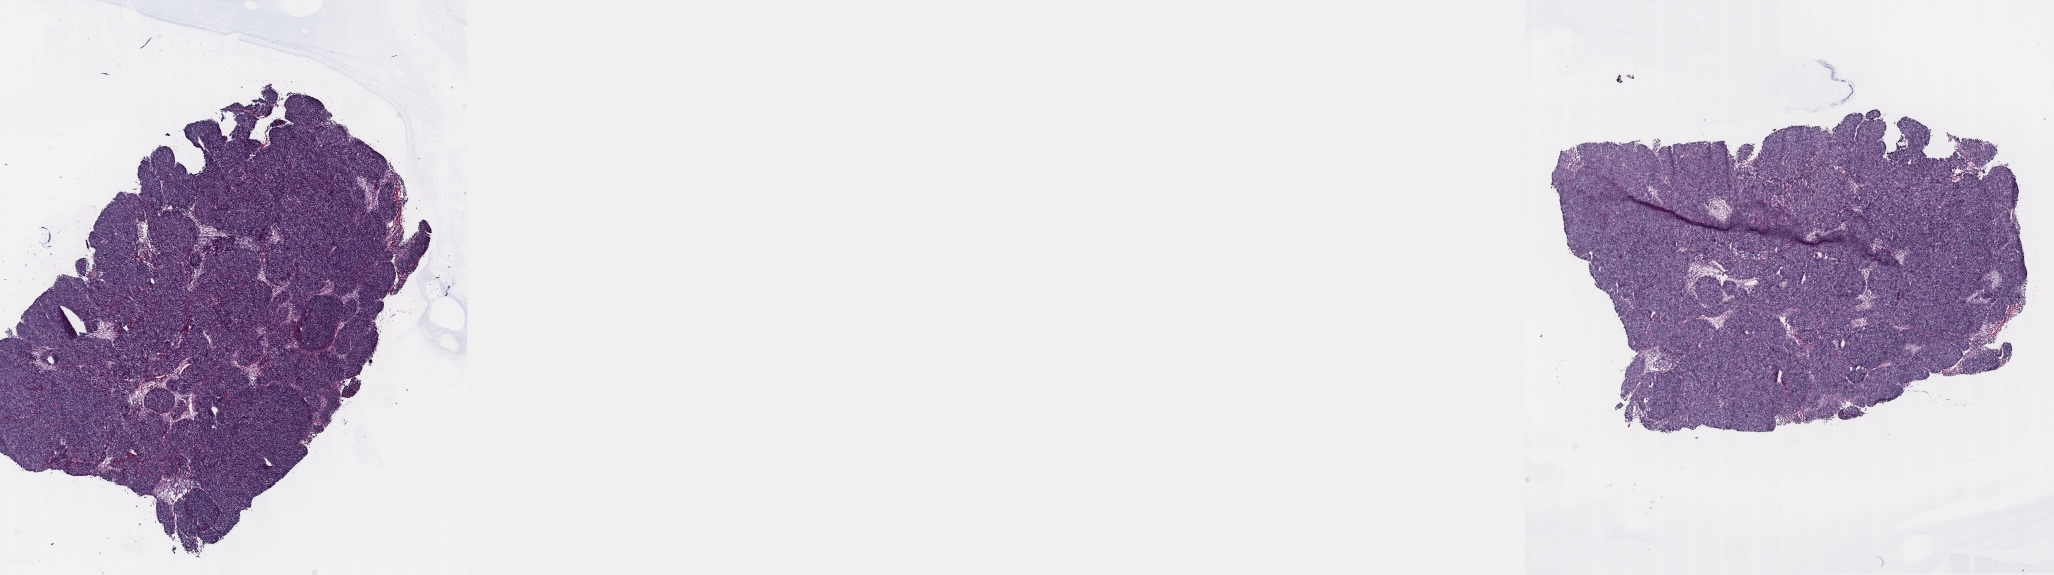
Whole-slide histology image, Hematoxylin and eosin (H&E) stained, whole scanned area (about 33.2 x 9.3 mm, acquisition: 40x scan) shown as a low-resolution overview, frozen section from the top of the tissue portion, sample: primary tumour, thymus. Patient: male, age at initial diagnosis 41 years. Pathologist review of this section (percent, as recorded): tumour cells 100%, tumour nuclei 80%, normal cells 0%, stromal cells 0%, necrosis 0%. Infiltration values recorded for this section: lymphocyte infiltration 2%, monocyte infiltration 0%, neutrophil infiltration 0%.
- histologic diagnosis: Thymoma, type B2, malignant (mediastinum, NOS)